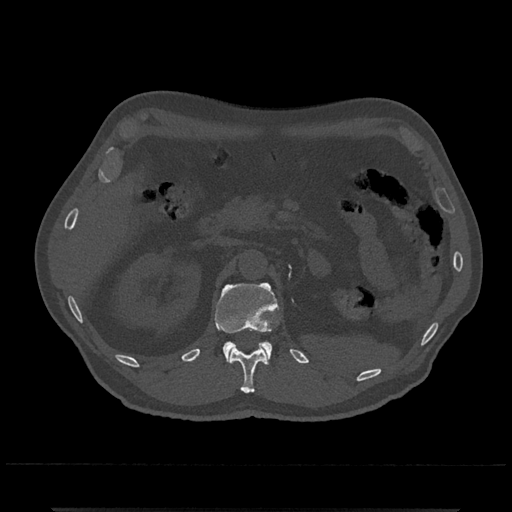
CT including the spine, one axial slice; position 396 of 797 along the scan axis; 120 kVp; bone window (W 1800 / L 400 HU); 0.5 mm slice thickness; 512 × 512 image matrix, field of view 393 × 393 mm. Male patient, age 67 years. Case-level facts recorded for this patient, not image findings: primary cancer: prostate.
Structures marked on this image (semi-automatically segmented with operator editing):
- L1 vertebra: box from (x=214, y=282) to (x=279, y=364) px
- T12 vertebra: (x=230, y=346)–(x=268, y=394)